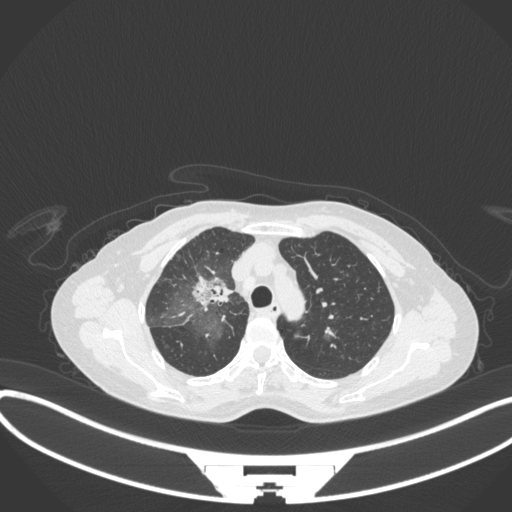
Chest CT, one axial slice; position 239 of 311 along the scan axis; reconstruction kernel B31f; 120 kVp; lung window (W 1500 / L -600 HU); 512 × 512 image matrix, field of view 400 × 400 mm. Female patient, age 59 years. From the clinical record (not read from this slice): clinical TNM (as recorded): T3 N0 M0.
Outlined on this slice (bounding box drawn by a radiologist):
- lung tumour (recorded histology: adenocarcinoma): bounding box <188,269,234,311> (left, top, right, bottom; pixels)